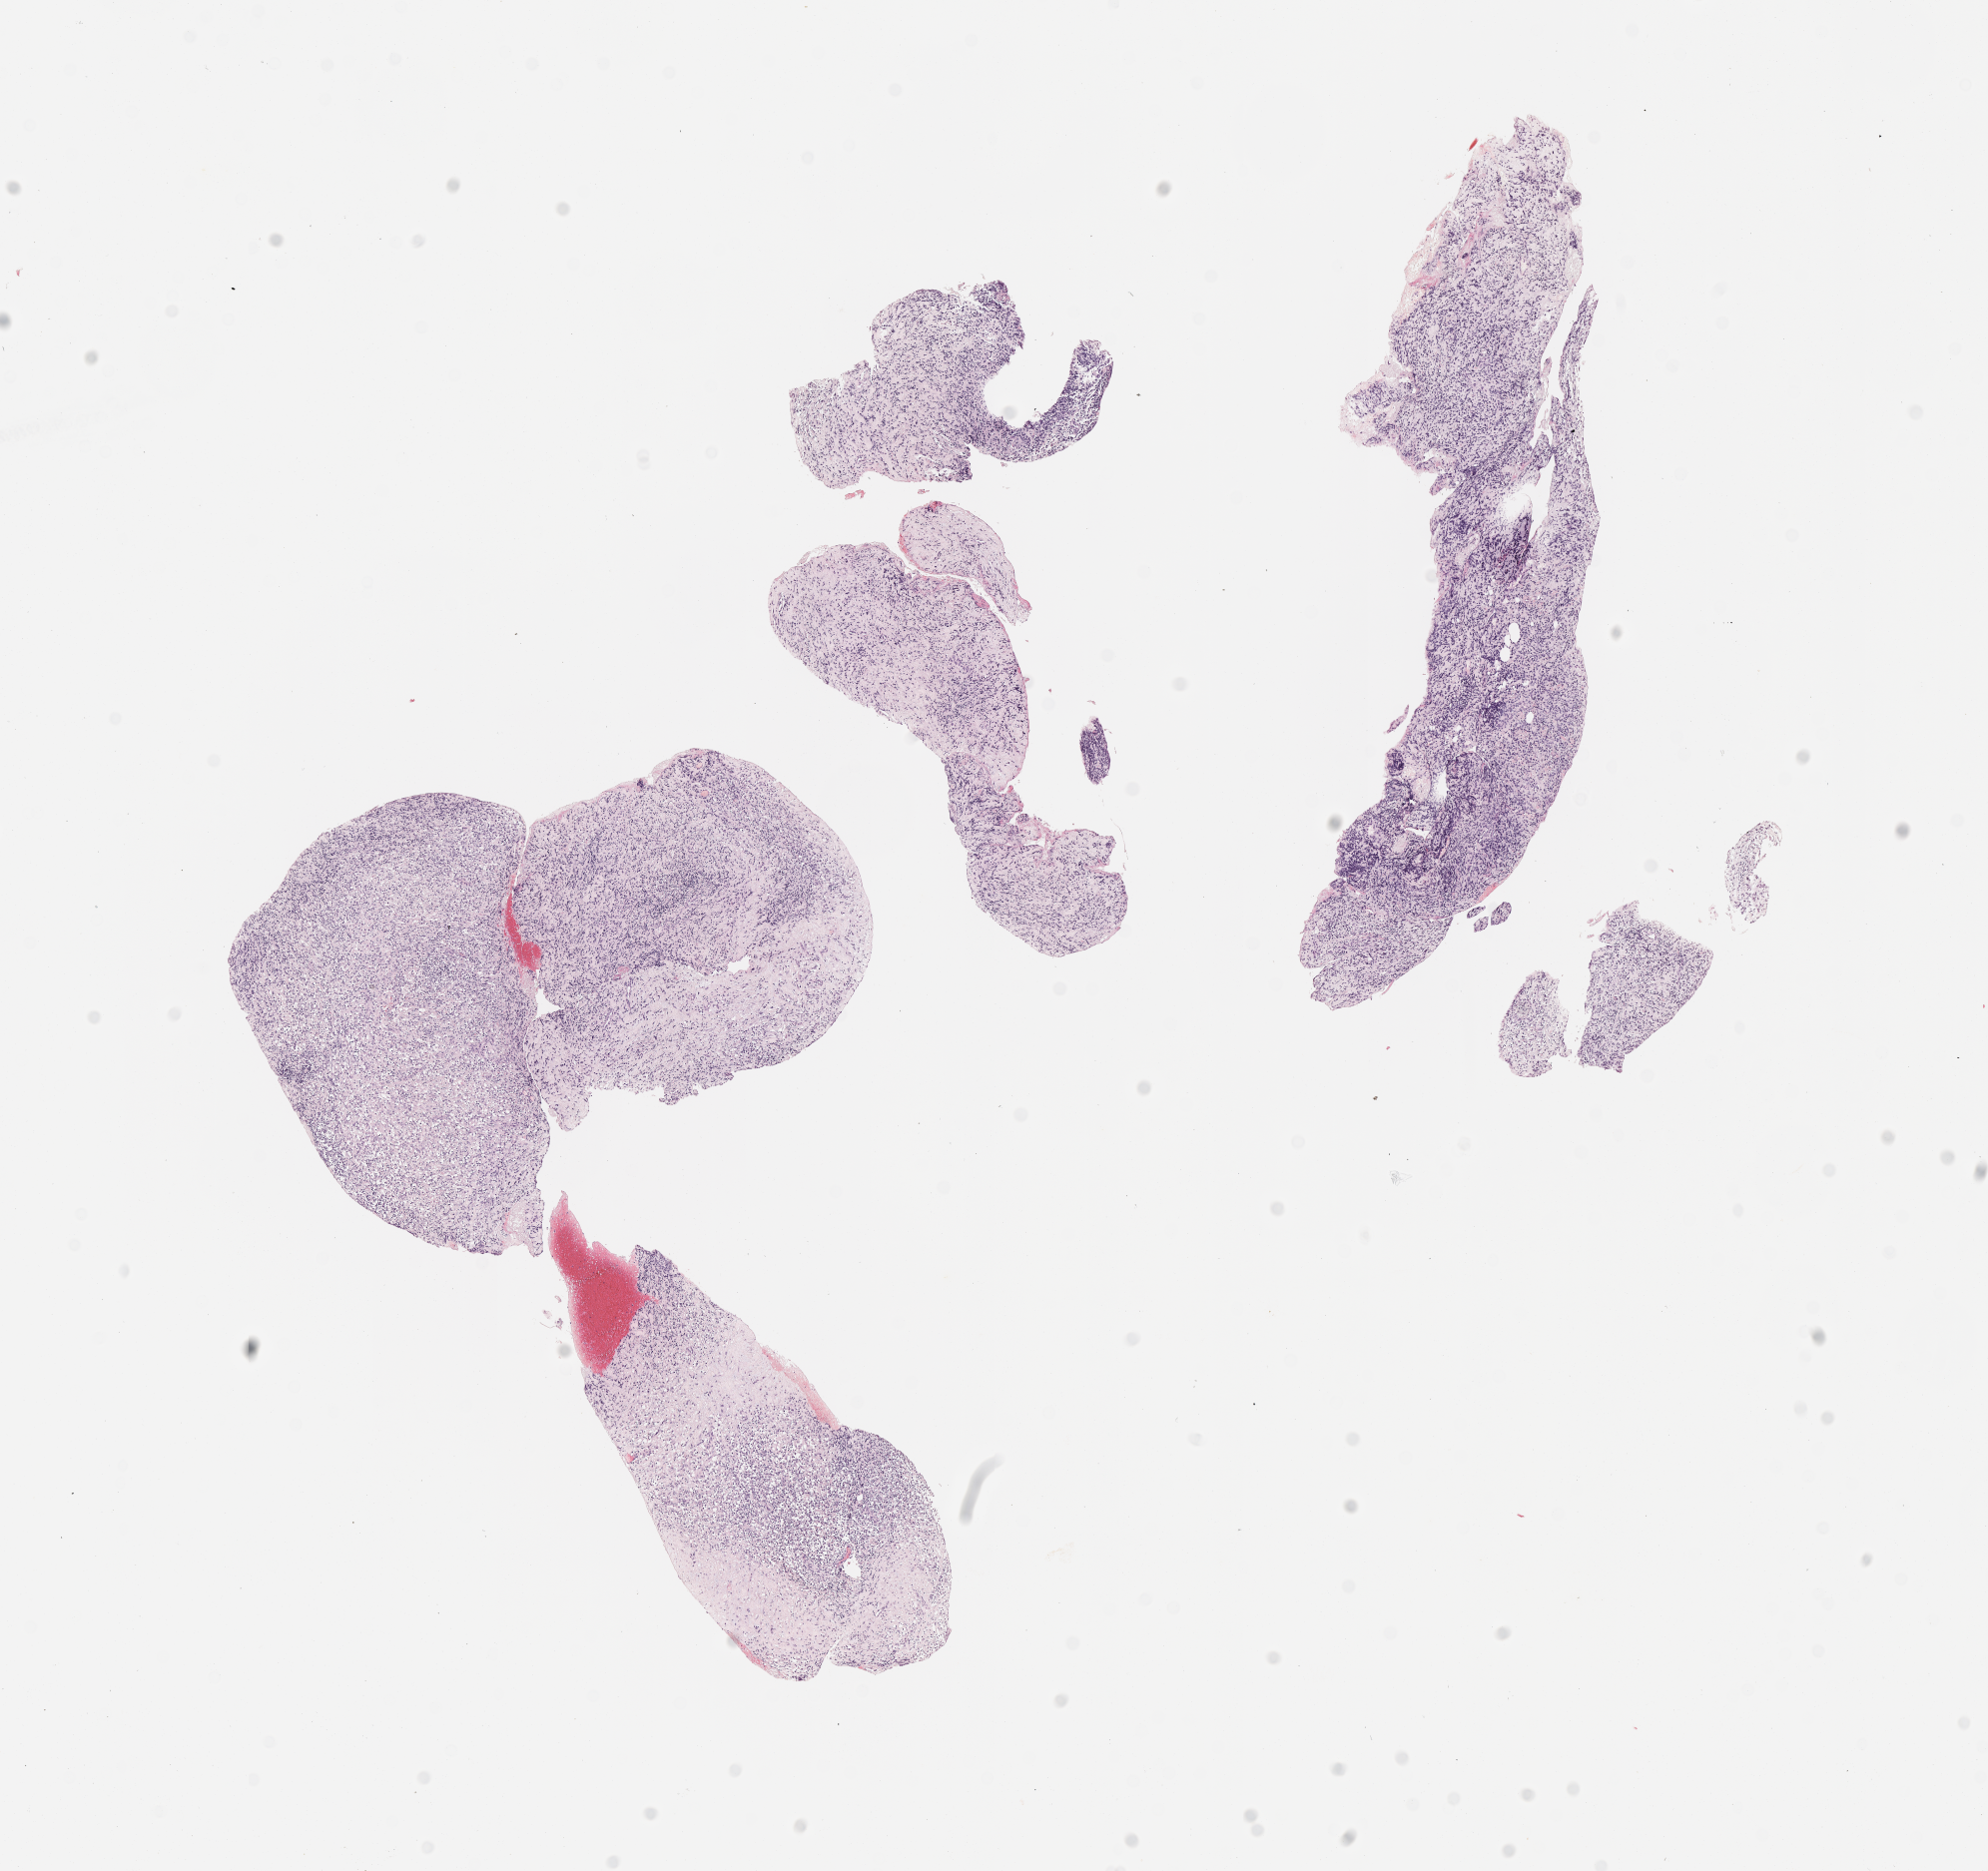
Whole-slide image, H&E stain of tumor tissue, a low-resolution overview of the entire scanned area, about 8.1 x 7.6 mm; FFPE section; site: perineum. Patient: male, age 0.1 years at diagnosis.
Metastatic status at presentation (as recorded): non-metastatic (unconfirmed). Stage (as recorded): 2. Diagnosis: rhabdomyosarcoma; histological classification: embryonal rhabdomyosarcoma.